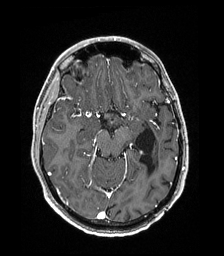
Brain MRI from a brain-tumour surgery series, one axial slice. Slice 111 of 192 in the series (ordered by position). T1-weighted post-contrast. 1 mm slice thickness. 224 × 256 image matrix. From the clinical record (not read from this slice): histopathology: Low grade glioma; IDH mutation: no.
Outlined on this slice (outlined manually by an expert reader):
- previous resection cavity: bounding box <134,128,156,174> (left, top, right, bottom; pixels)